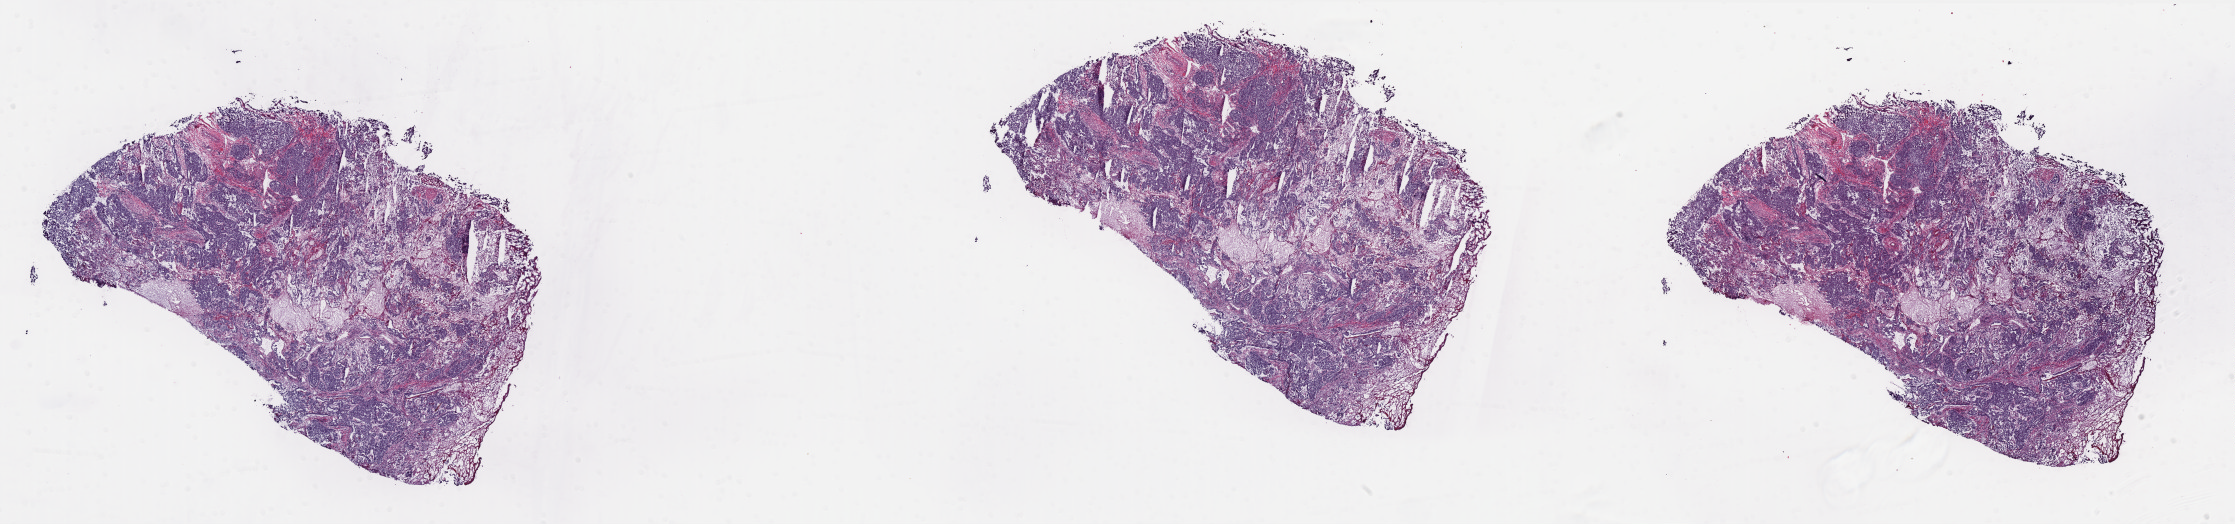
Digitized H&E tissue section (whole slide), low-resolution overview of the scanned area, about 35.8 x 8.4 mm. Frozen section from the bottom of the tissue portion. Uterus, primary tumour sample. Female patient; age at initial diagnosis 69 years. Histologic grade: G3 (poorly differentiated). Composition of this section per pathologist review: tumour cells 60%, tumour nuclei 75%, normal cells 0%, stromal cells 15%, necrosis 25%. Inflammatory infiltration, as recorded: lymphocyte infiltration 0%, monocyte infiltration 0%, neutrophil infiltration 0%.
Pathologic diagnosis: Serous cystadenocarcinoma, NOS (endometrium). FIGO stage: IIIC.